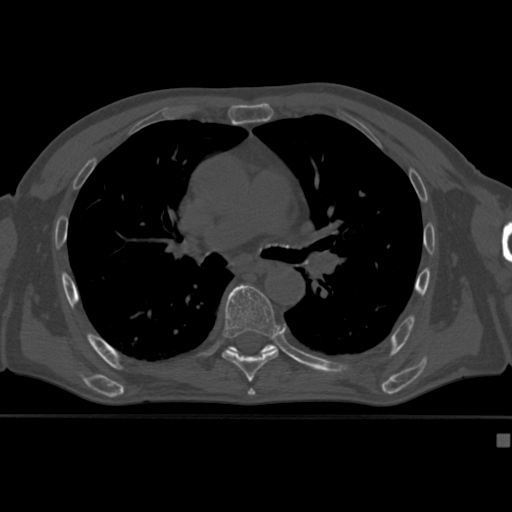
CT including the spine, one axial slice. Position 277 of 430 along the scan axis. Reconstruction kernel Br40s. Bone window (W 1800 / L 400 HU). 1.5 mm slice thickness. 512 × 512 image matrix, field of view 337 × 337 mm. Patient: male, 64 years. From the clinical record (not read from this slice): primary cancer: uterus.
Outlined on this slice (semi-automatically segmented with operator editing):
- T7 vertebra: bounding box [x1, y1, x2, y2] px = [222, 284, 279, 382]
- T8 vertebra: [229, 345, 276, 359]